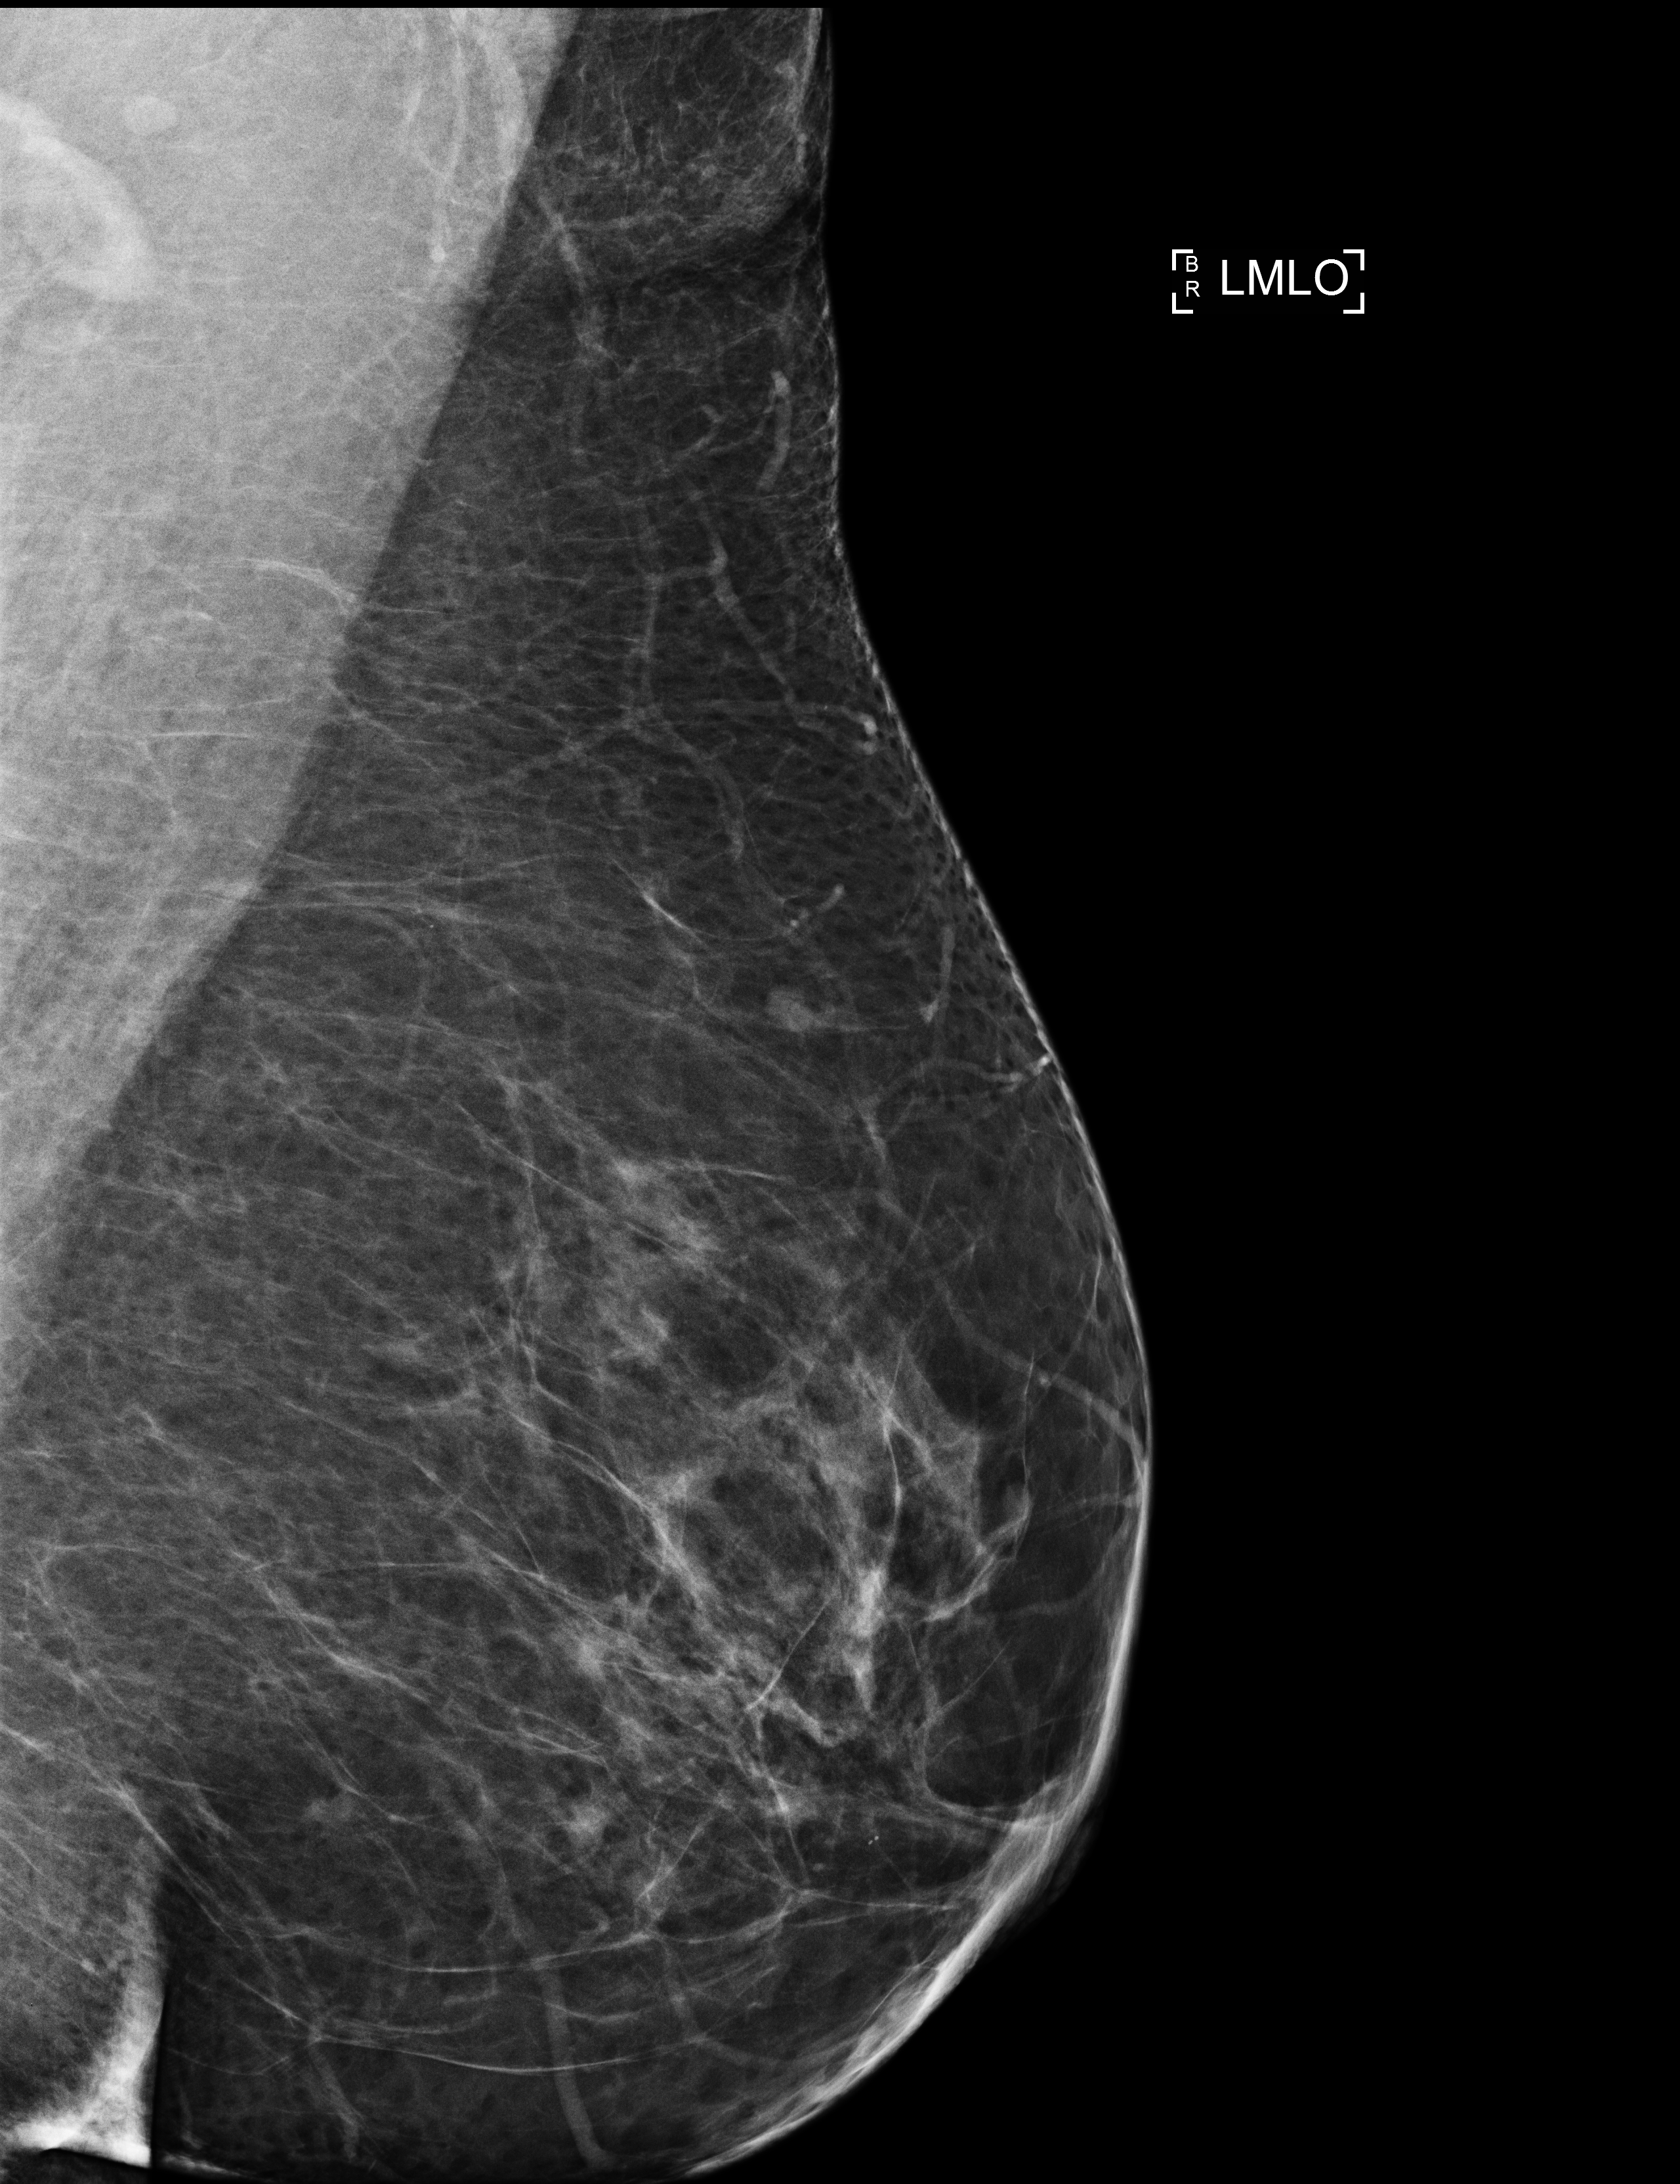
Digital mammogram (FFDM); left breast; medio-lateral oblique projection; screening examination. Female patient, age 44 years.
Breast density at the screening exam (both breasts): scattered fibroglandular densities (BI-RADS density category b). Final BI-RADS category for the screening round (tomosynthesis exam, both breasts): category 2. Recall: no recall after this screen.